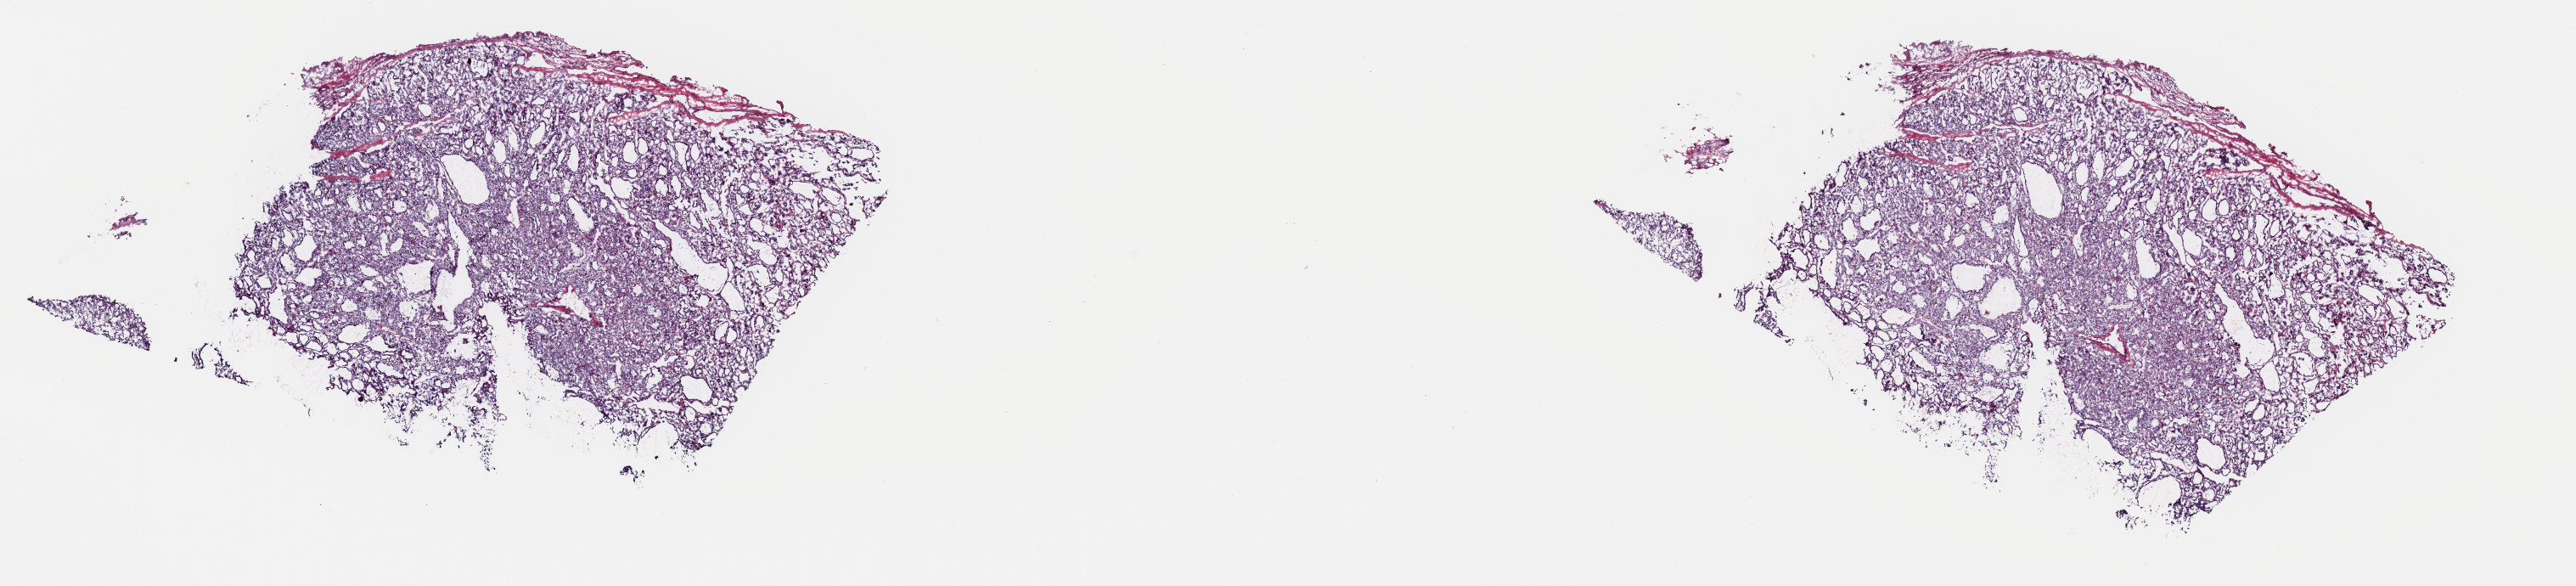
Digitized Hematoxylin and eosin (H&E) stained tissue section (whole slide) — shown as a low-resolution overview of the whole scanned area (about 24.0 x 5.5 mm, slide scanned at 40x); frozen section from the top of the tissue portion; primary tumour sample from the thyroid. Female, age 55 years at initial diagnosis. Slide review estimates, as recorded: tumour cells 95%, tumour nuclei 95%, normal cells 0%, stromal cells 5%, necrosis 0%. Inflammatory infiltration, as recorded: lymphocyte infiltration 1%, monocyte infiltration 0%, neutrophil infiltration 0%.
• laterality: right
• AJCC pathologic stage: III
• pathologic diagnosis: Papillary carcinoma, follicular variant (thyroid gland)
• lymph nodes positive (case pathology): 0 of 1 examined